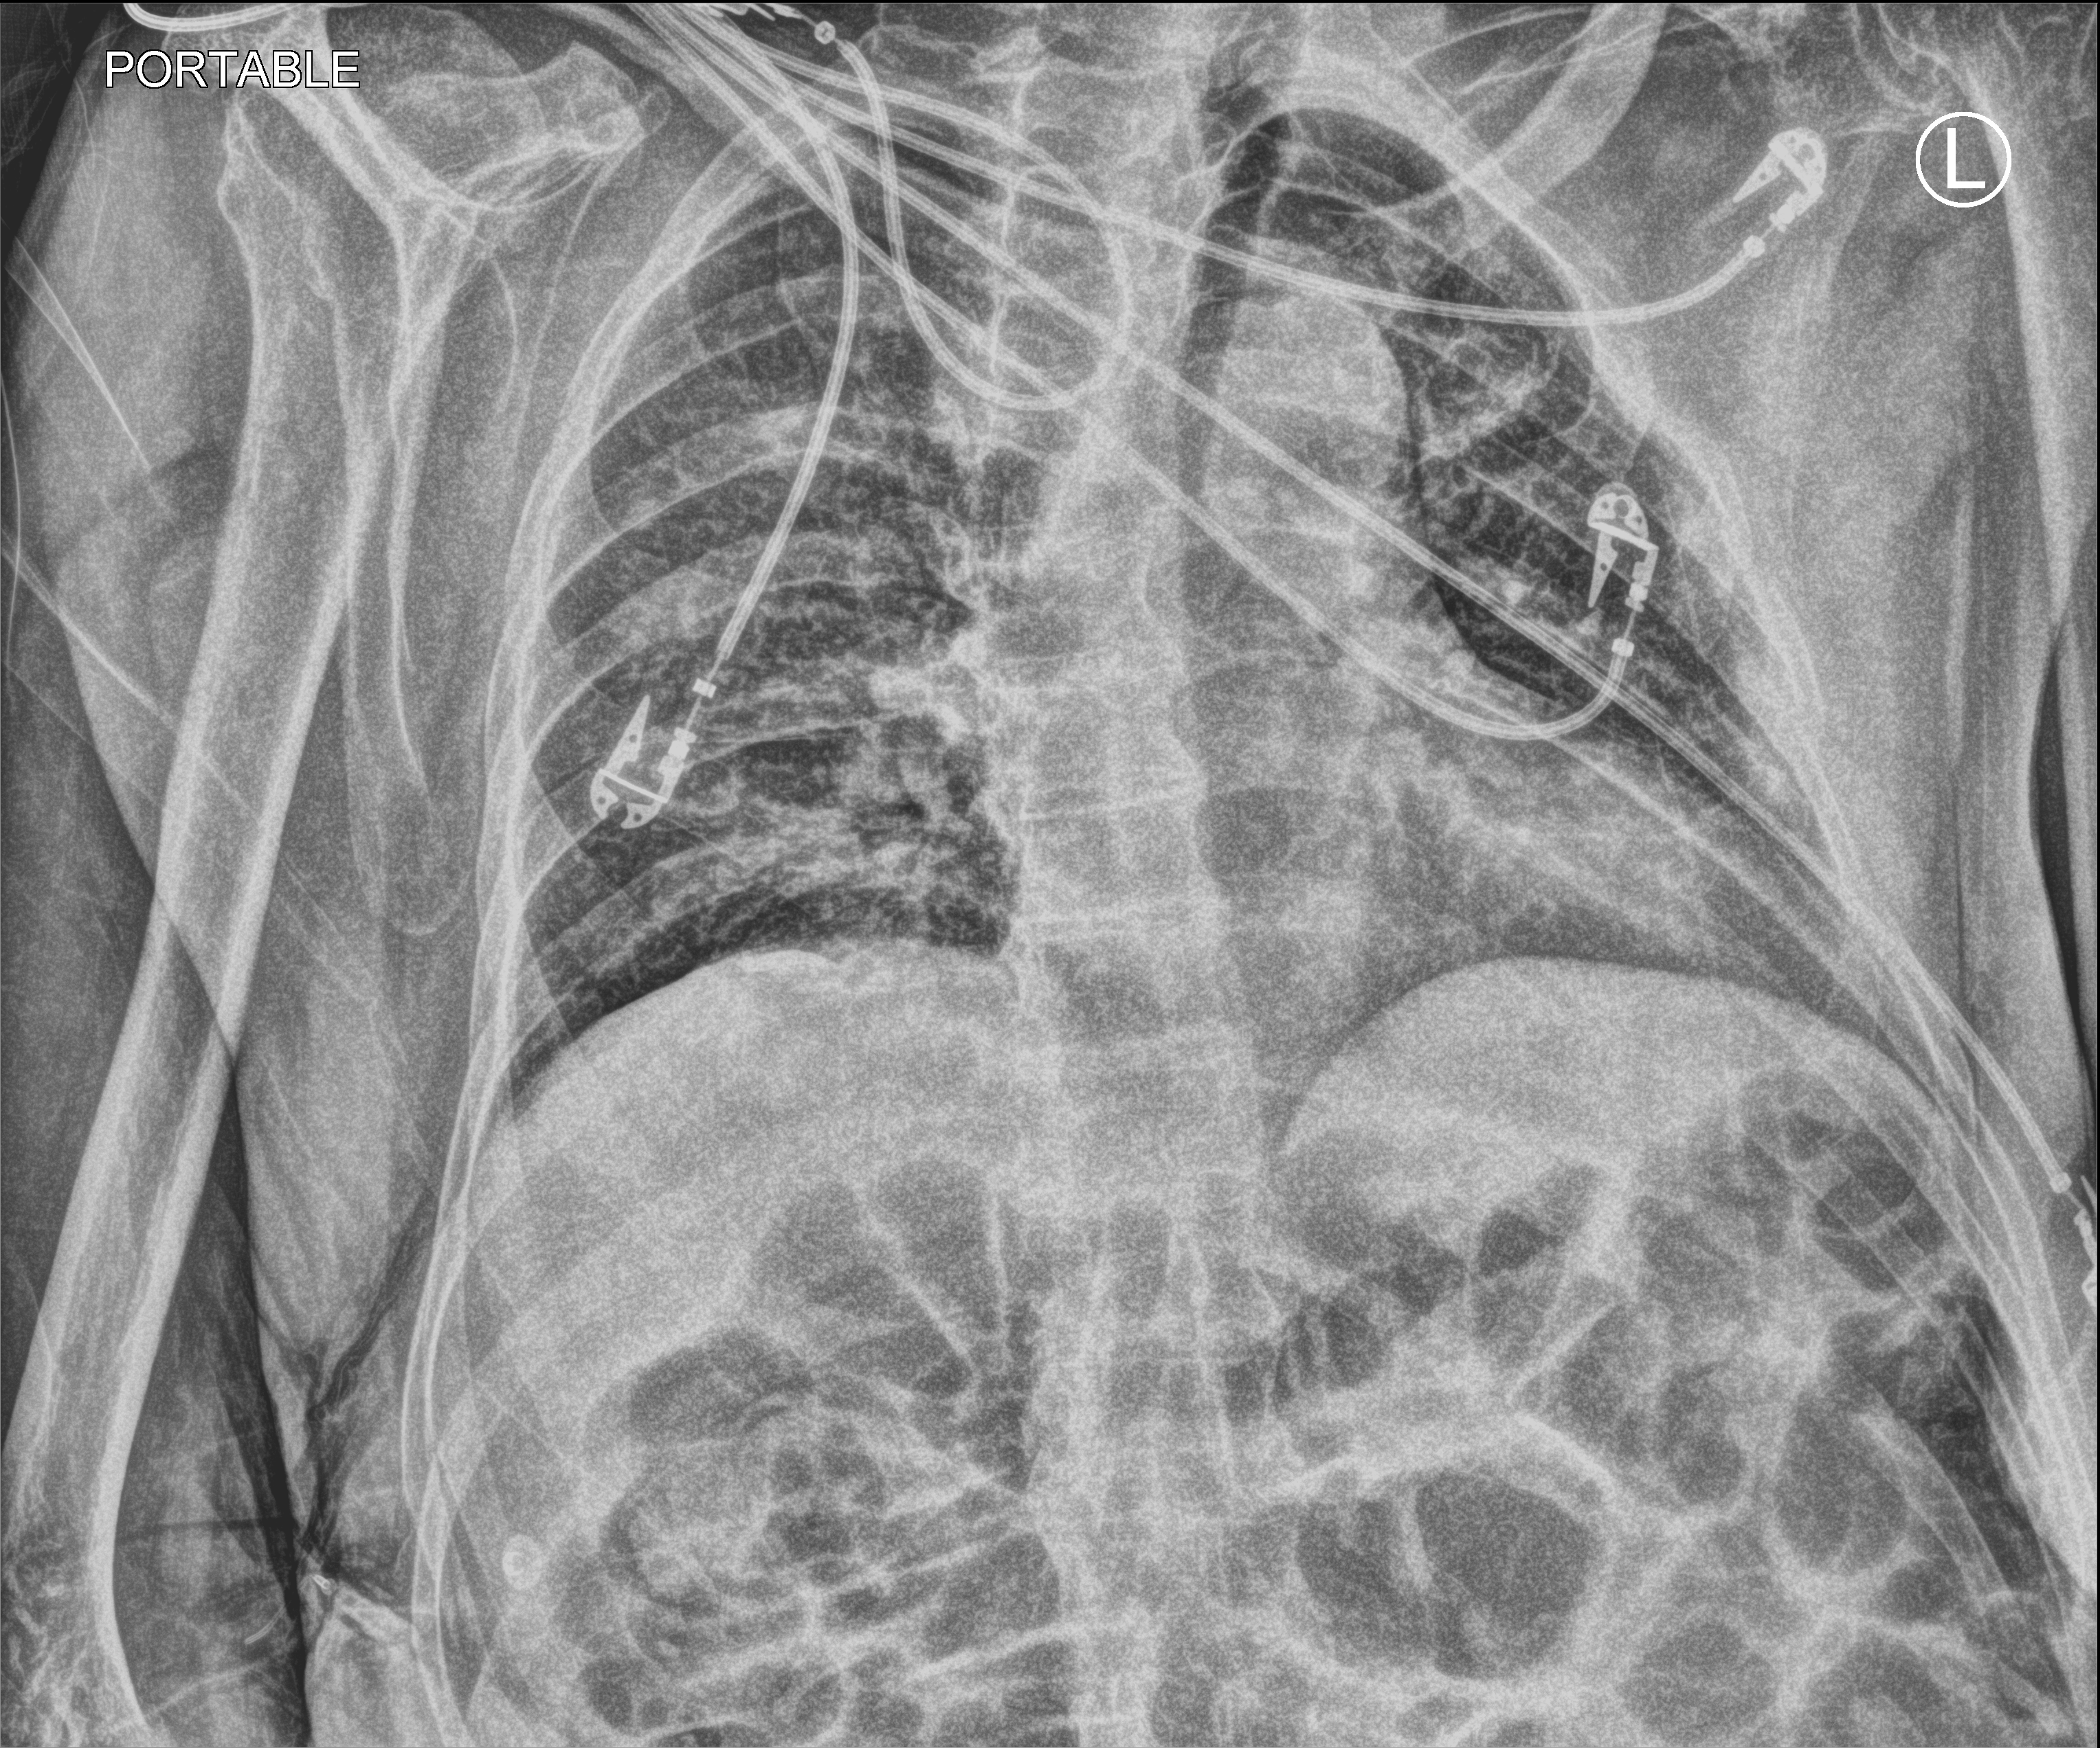
Portable chest radiograph; anteroposterior (AP) projection. Patient hospitalised with COVID-19; male, aged 75–90 years.
Admission-level facts for this patient (not findings on this image; timing relative to this image not recorded): admitted to intensive care during this hospital stay: no; mechanically ventilated during this hospital stay: no; length of hospital stay: 1 day.